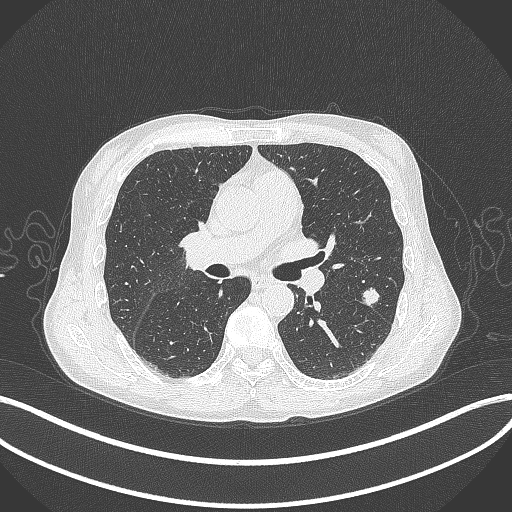
Chest CT, one axial slice. 120 kVp. Lung window (W 1500 / L -600 HU). 1 mm slice thickness. 512 × 512 image matrix, field of view 400 × 400 mm. Male patient, age 58 years. Case-level facts recorded for this patient, not image findings: clinical TNM (as recorded): T1c N0 M0; histopathological grade: G2.
Outlined on this slice (rectangle marked by the reading radiologist):
- lung tumour (recorded histology: adenocarcinoma): bounding box (x1, y1, x2, y2) in pixels: (360, 283, 381, 307)